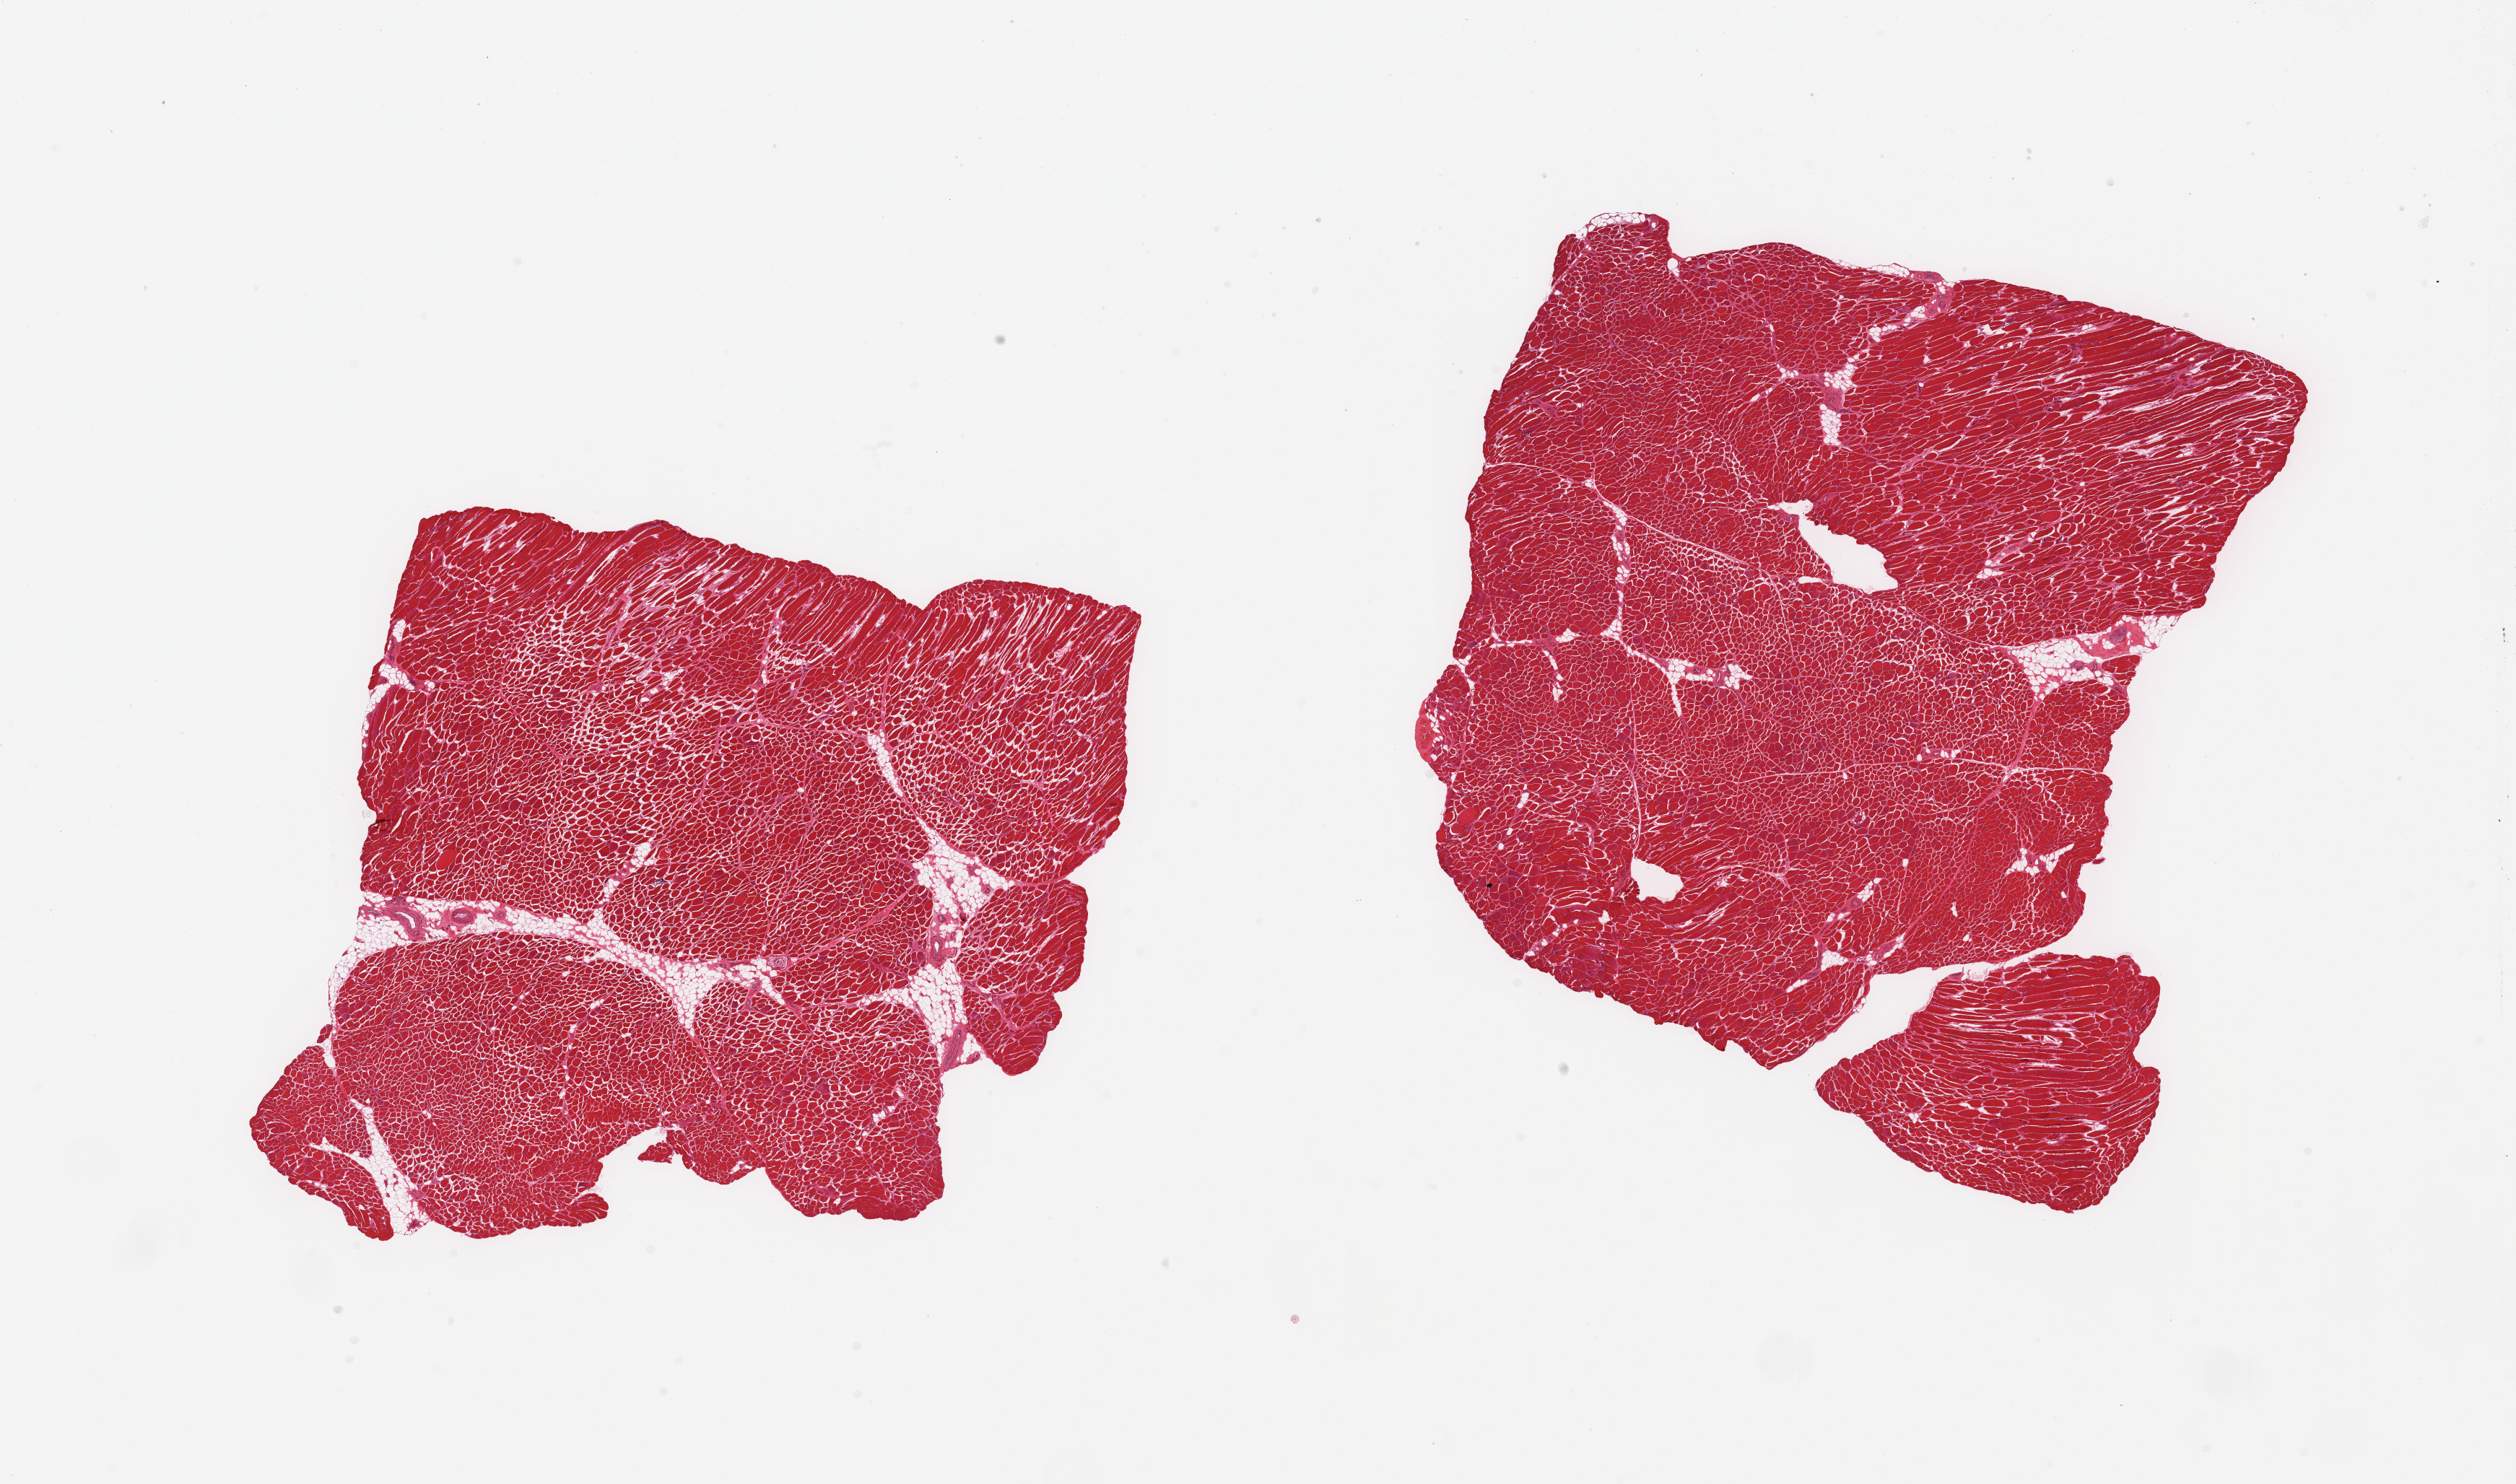
Whole-slide image, haematoxylin and eosin stain — whole scanned area (about 27.6 x 16.3 mm, slide scanned at 20x) shown as a low-resolution overview. PAXgene-fixed paraffin-embedded (PFPE) section. Section of skeletal muscle (target tissue). Tissue donor sample. Male donor.
Pathologist's review note for this sample: 2 pieces; 5% internal fat content.